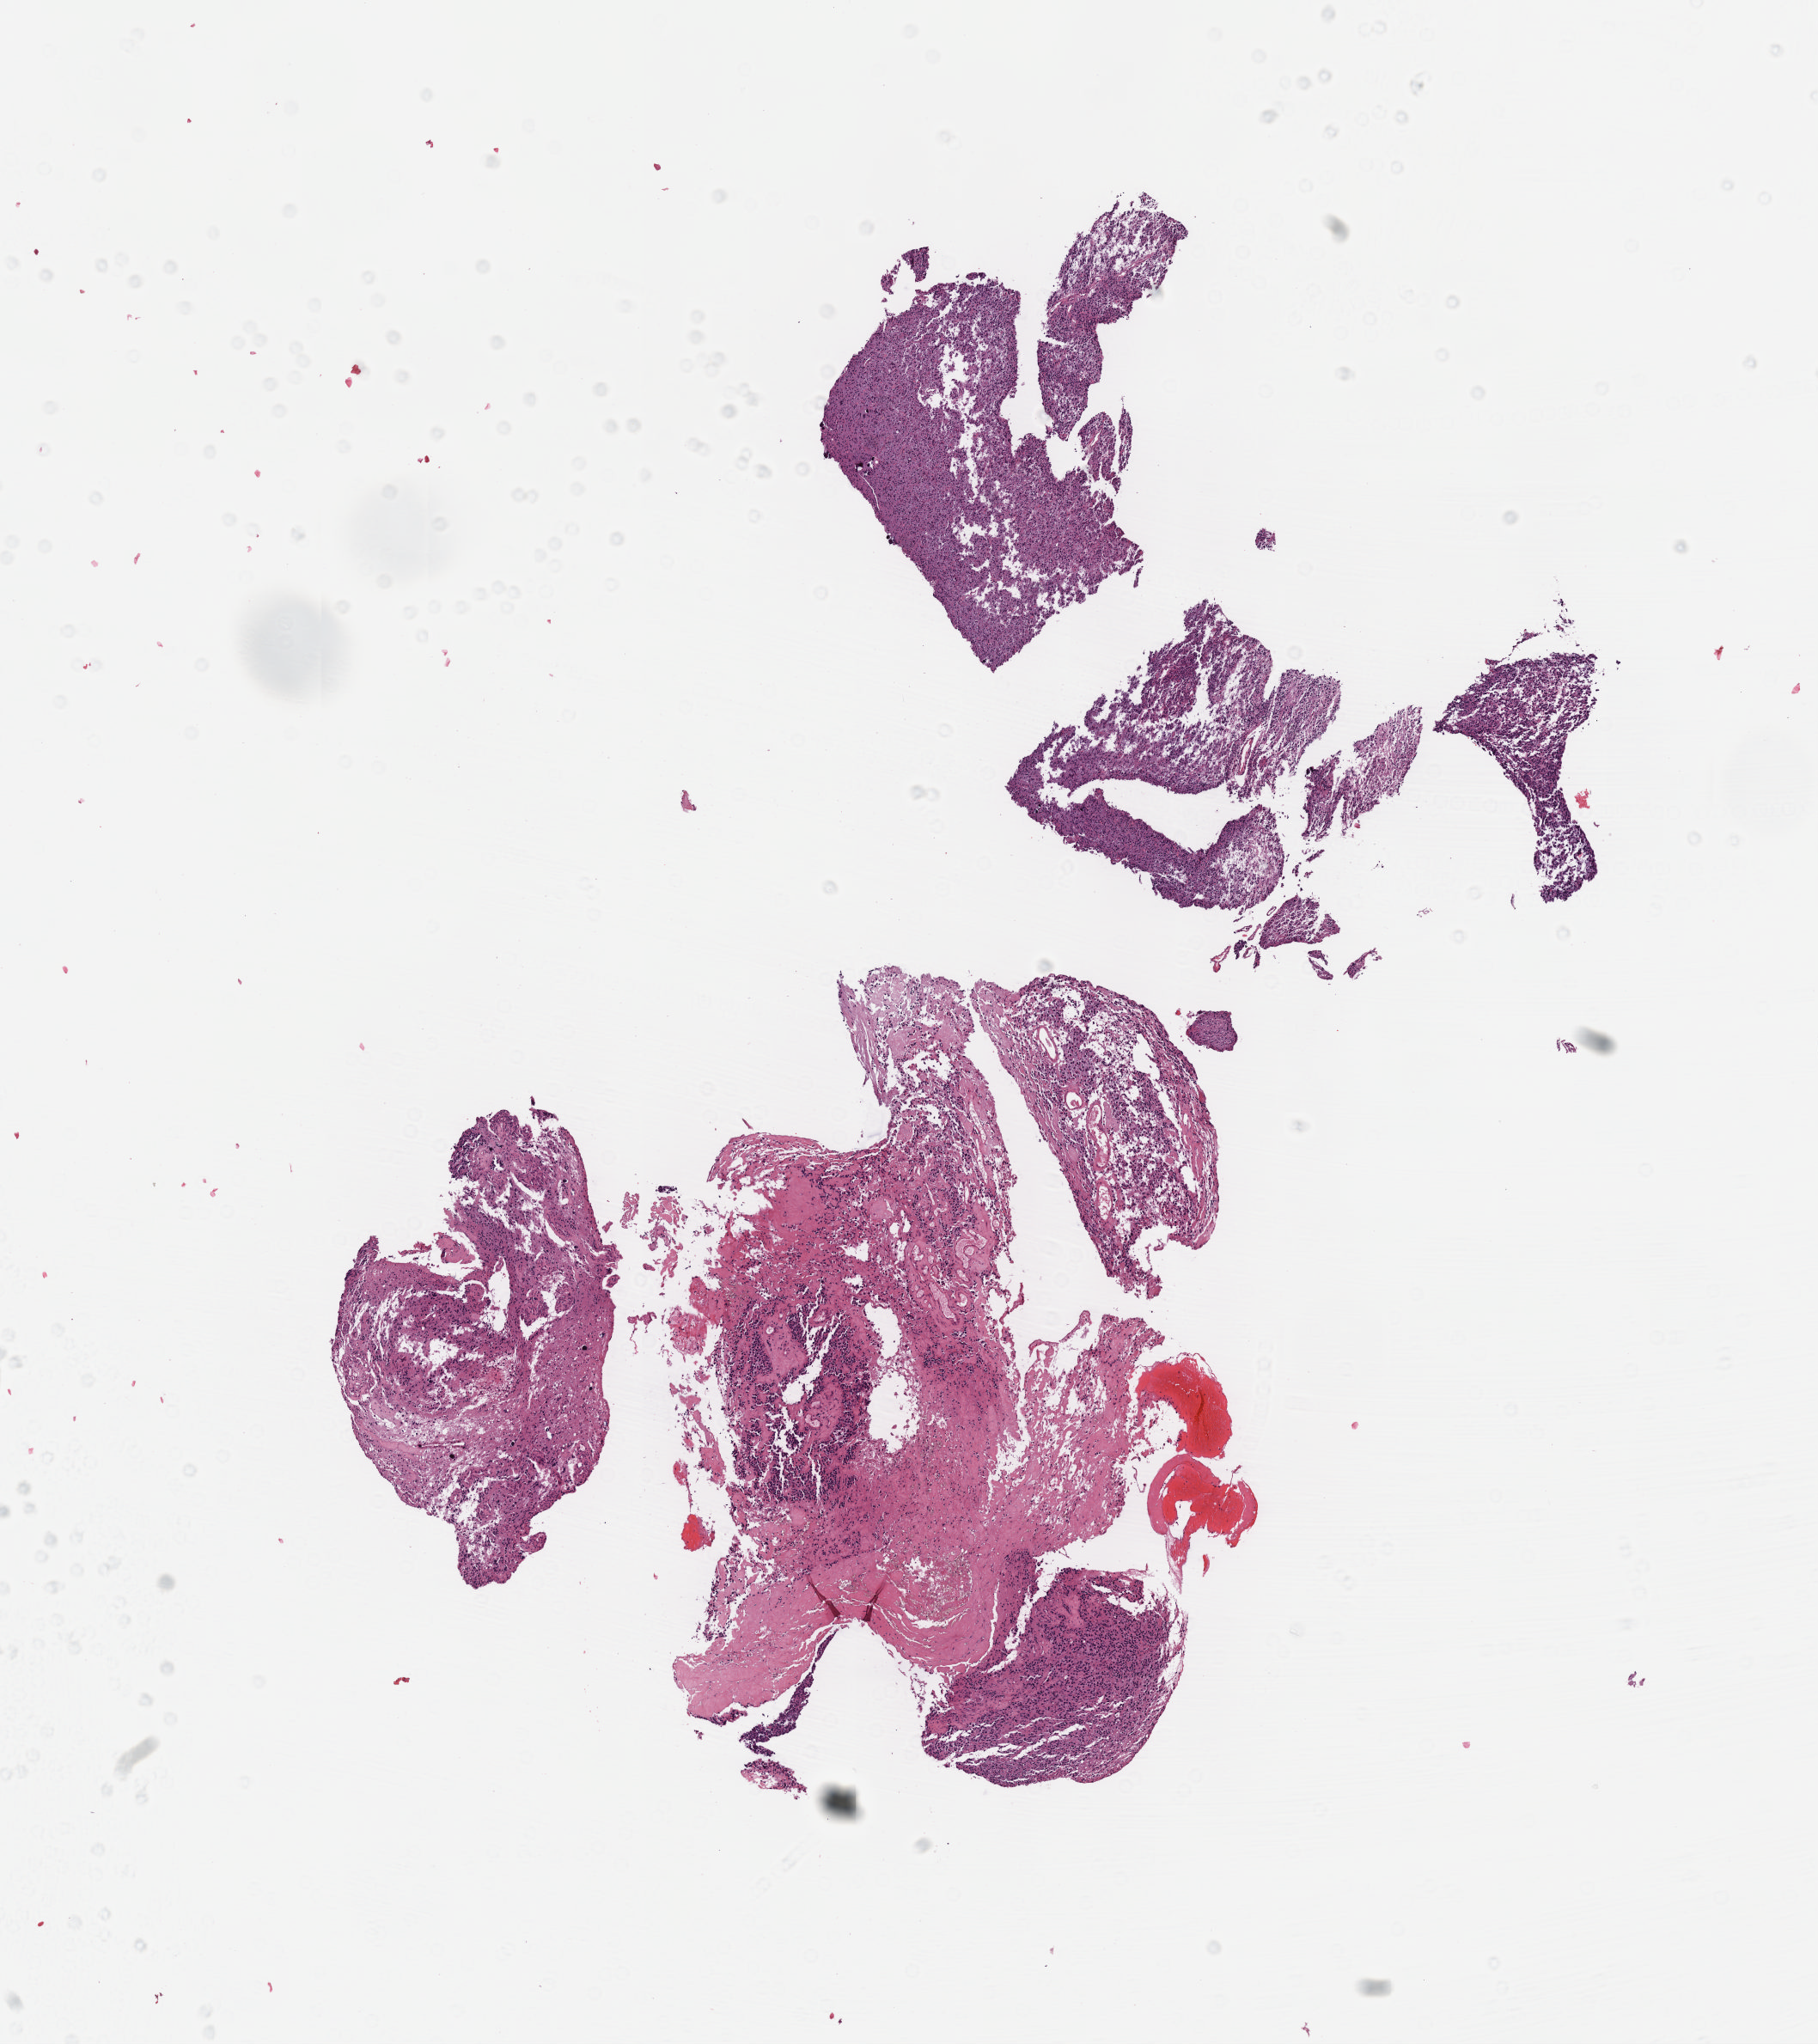
Digitized Hematoxylin and eosin (H&E) stained tissue section (whole slide), shown as a low-resolution overview of the whole scanned area (about 8.6 x 9.6 mm), formalin-fixed paraffin-embedded (FFPE) diagnostic section, brain, primary tumour sample. Male patient; age at initial diagnosis 33 years. Histologic grade: G2 (moderately differentiated).
* pathologic diagnosis: Oligodendroglioma, NOS
* laterality: right